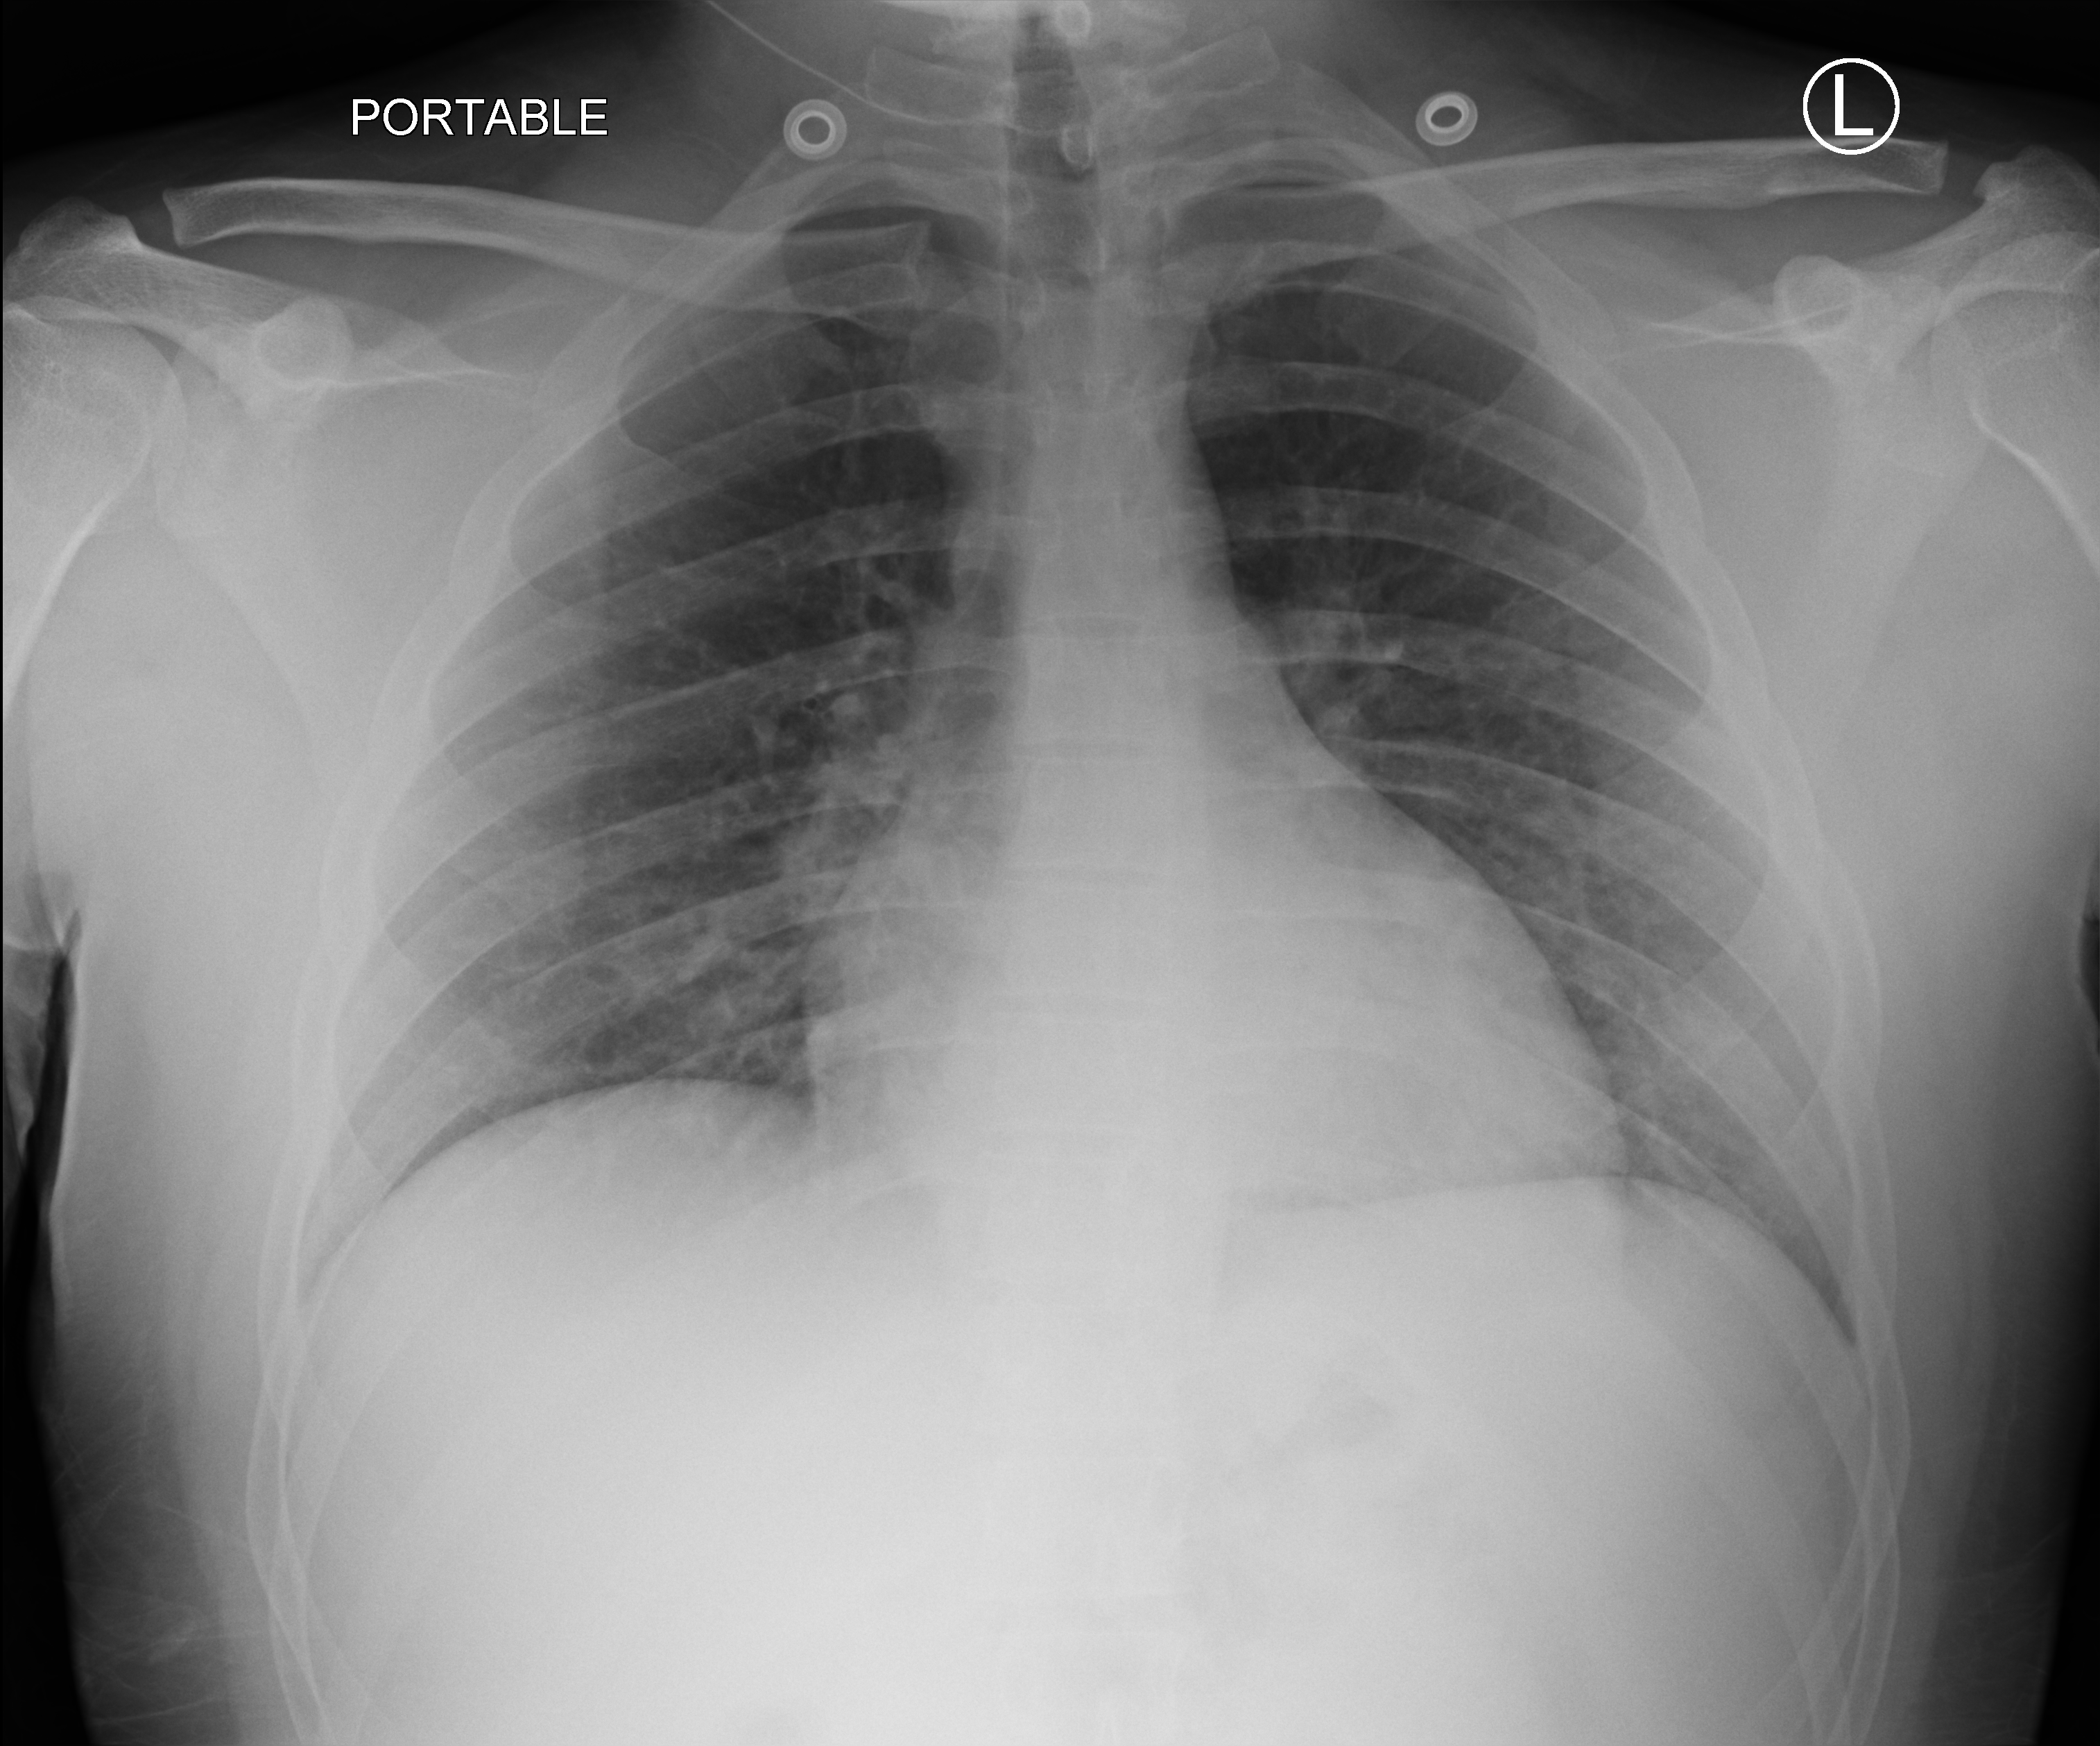
Bedside chest radiograph (computed radiography), anteroposterior (AP) projection. Patient hospitalised with COVID-19; male, aged 18–59 years.
Hospital-stay facts (about this admission, not read from this image; timing relative to this image not recorded): mechanically ventilated during this hospital stay: no; length of hospital stay: 1 day.